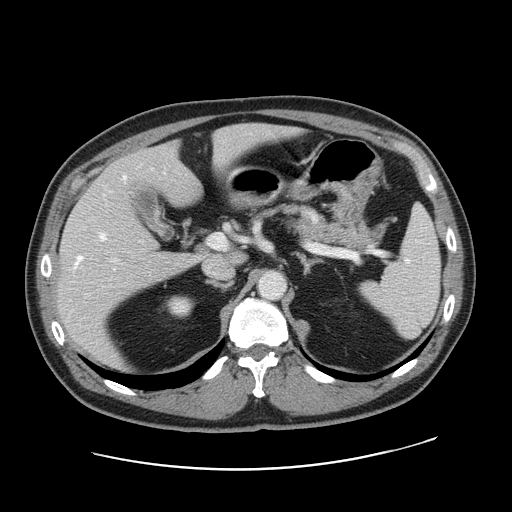
Contrast-enhanced abdominal CT, one axial slice. Slice 99 of 178 in the series (ordered by position). 120 kVp. Soft-tissue window (W 400 / L 40 HU). 512 × 512 image matrix. Male patient, age 63 years. Case-level facts recorded for this patient, not image findings: diagnosis: colorectal cancer liver metastases, imaged before liver resection; multiple liver metastases: yes; largest metastasis: 8 cm; disease in both lobes: yes.
Annotated regions visible in this slice (manually delineated by an expert):
- hepatic veins: bounding box <76,176,126,265> (left, top, right, bottom; pixels)
- liver: <57,124,288,364>
- planned liver remnant (the part of the liver to remain after resection): <120,124,290,206>
- portal vein (with intrahepatic branches): <112,234,226,261>